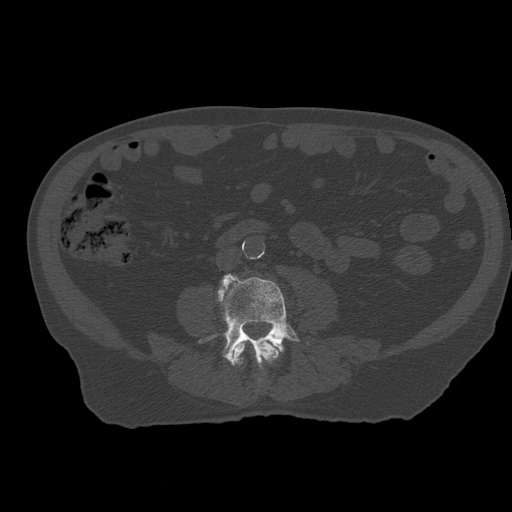
CT including the spine, one axial slice; position 170 of 399 along the scan axis; reconstruction kernel STANDARD; bone window (W 1800 / L 400 HU); 1.25 mm slice thickness; 512 × 512 image matrix, field of view 407 × 407 mm. Patient age 73 years. From the clinical record (not read from this slice): primary cancer: prostate.
Annotated regions visible in this slice (semi-automatic segmentation, software-assisted and operator-edited):
- L3 vertebra: bounding box (x1, y1, x2, y2) in pixels: (234, 341, 280, 383)
- L4 vertebra: (200, 273, 301, 366)